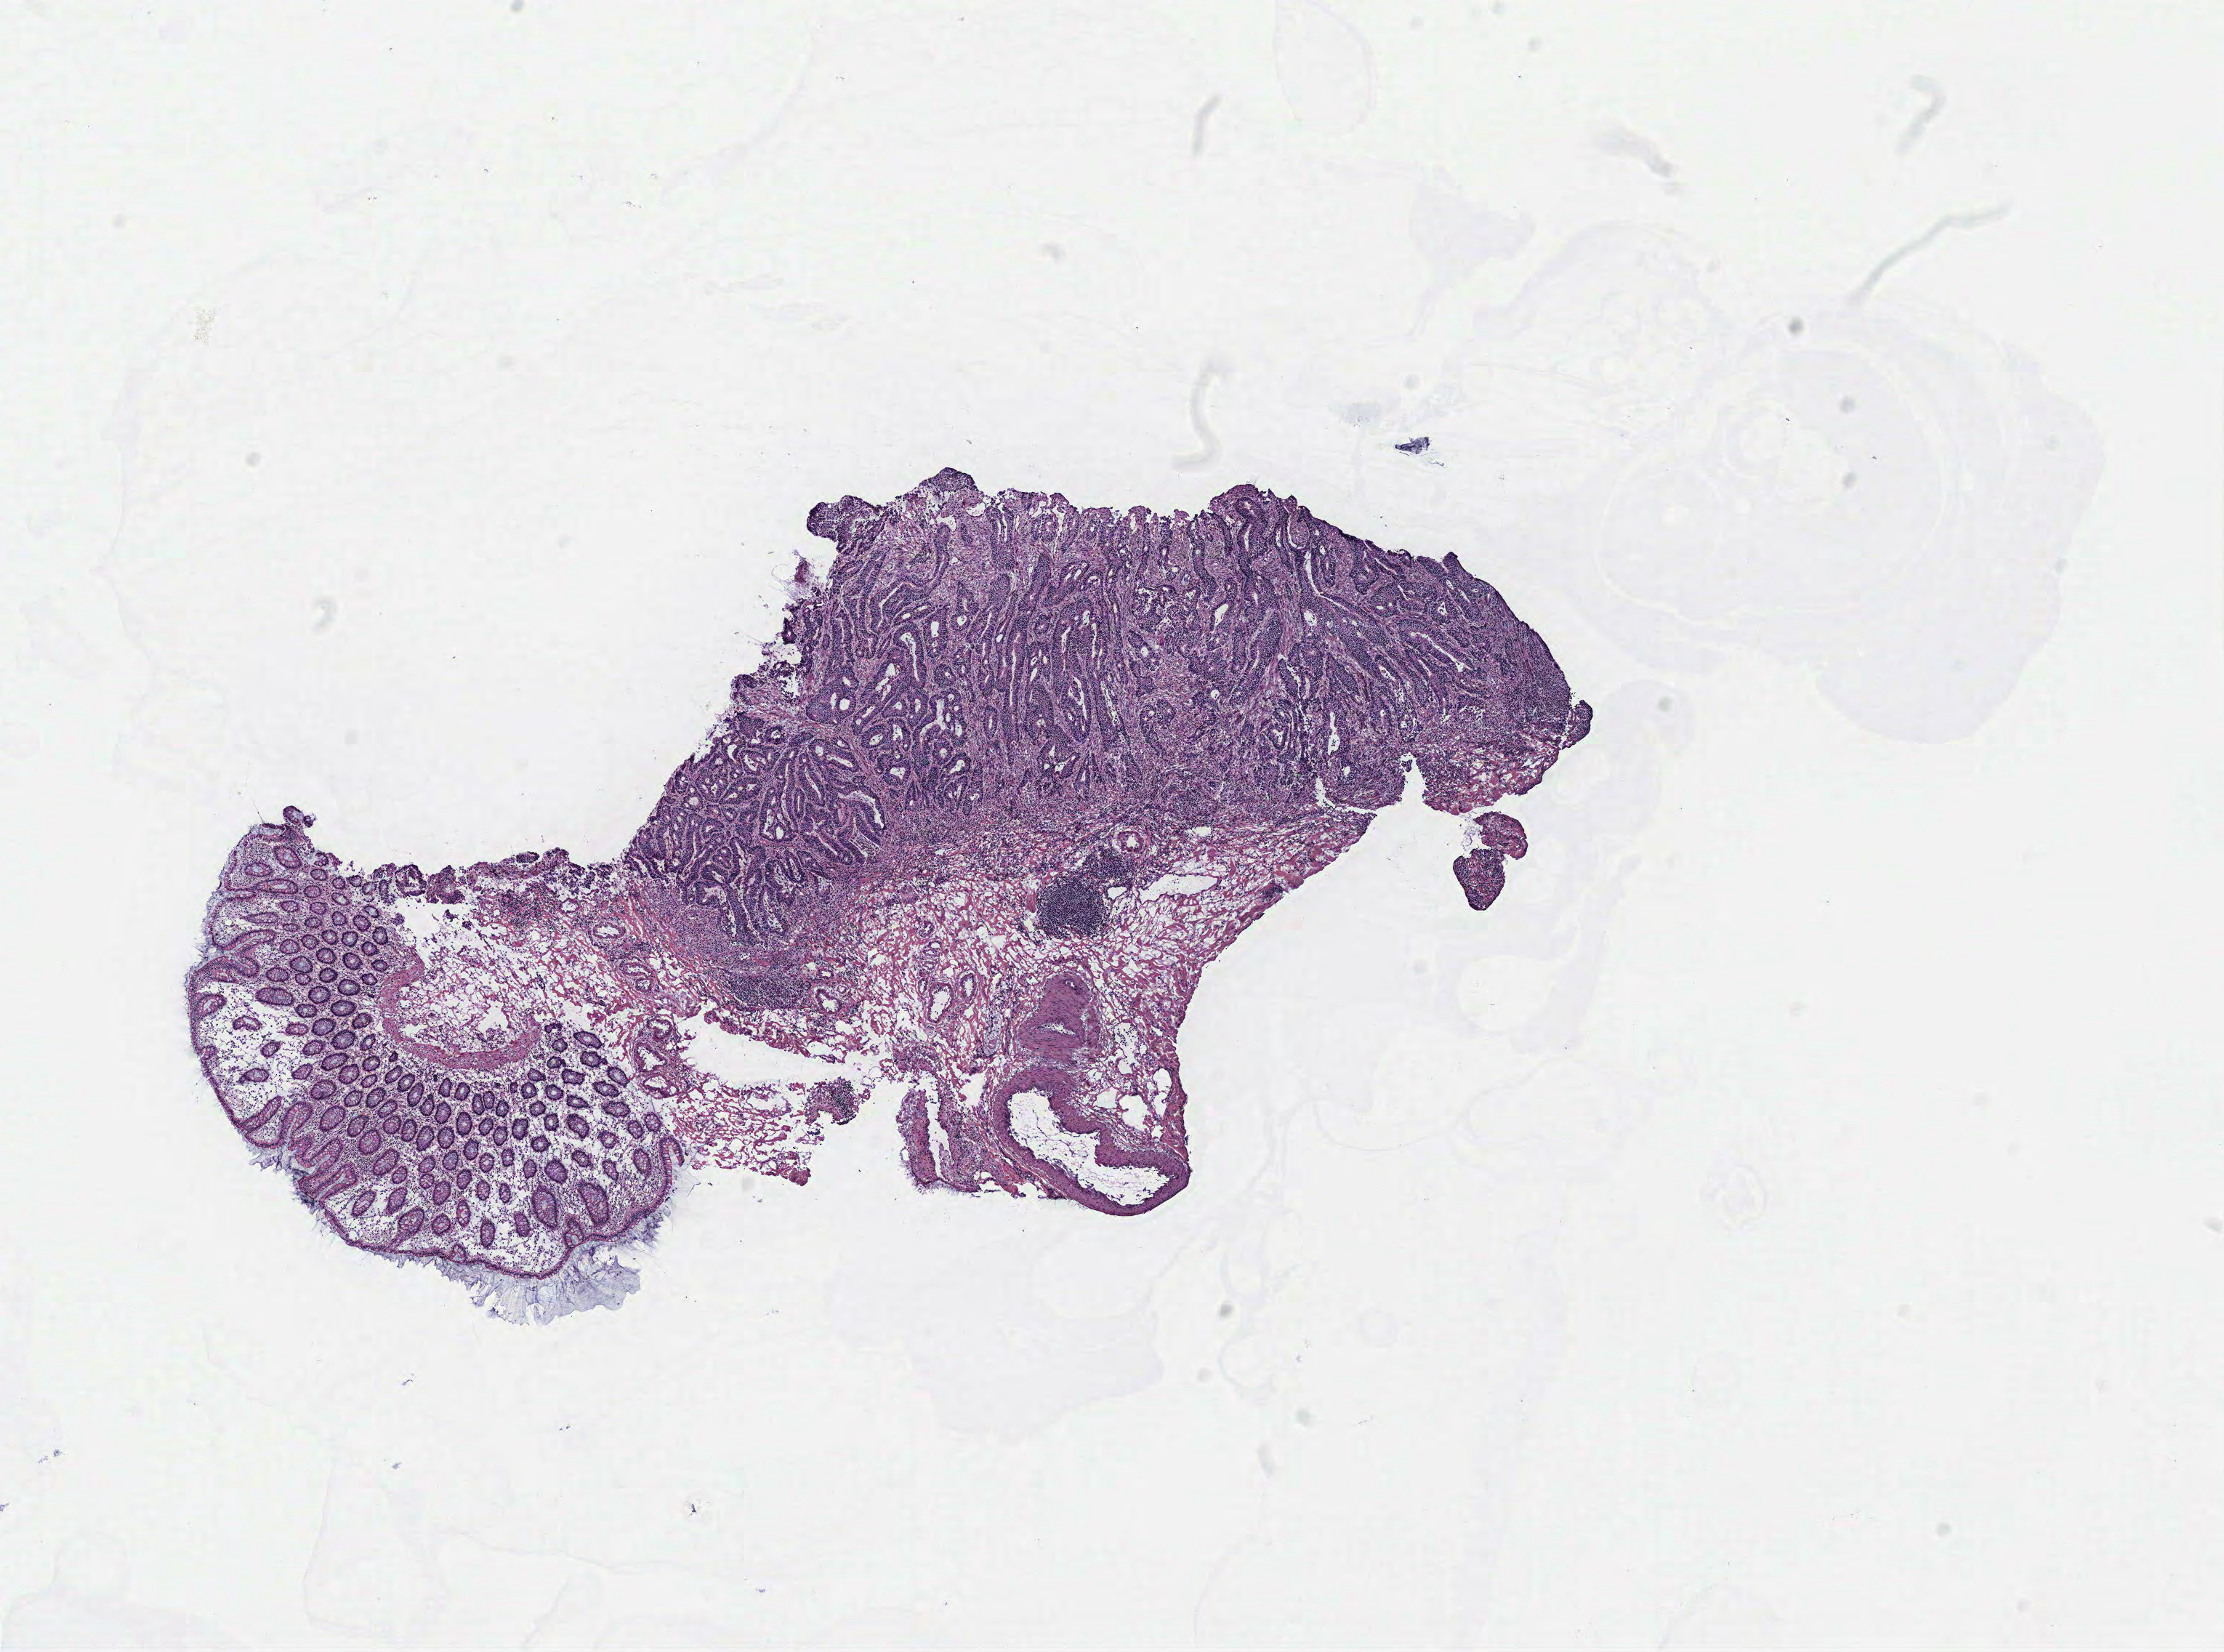
Hematoxylin and eosin (H&E) stained whole-slide image, shown as a low-resolution overview of the whole scanned area (about 12.2 x 9.1 mm); colon, tissue type not recorded. Male patient.
Patient diagnosis: Adenocarcinoma, NOS.